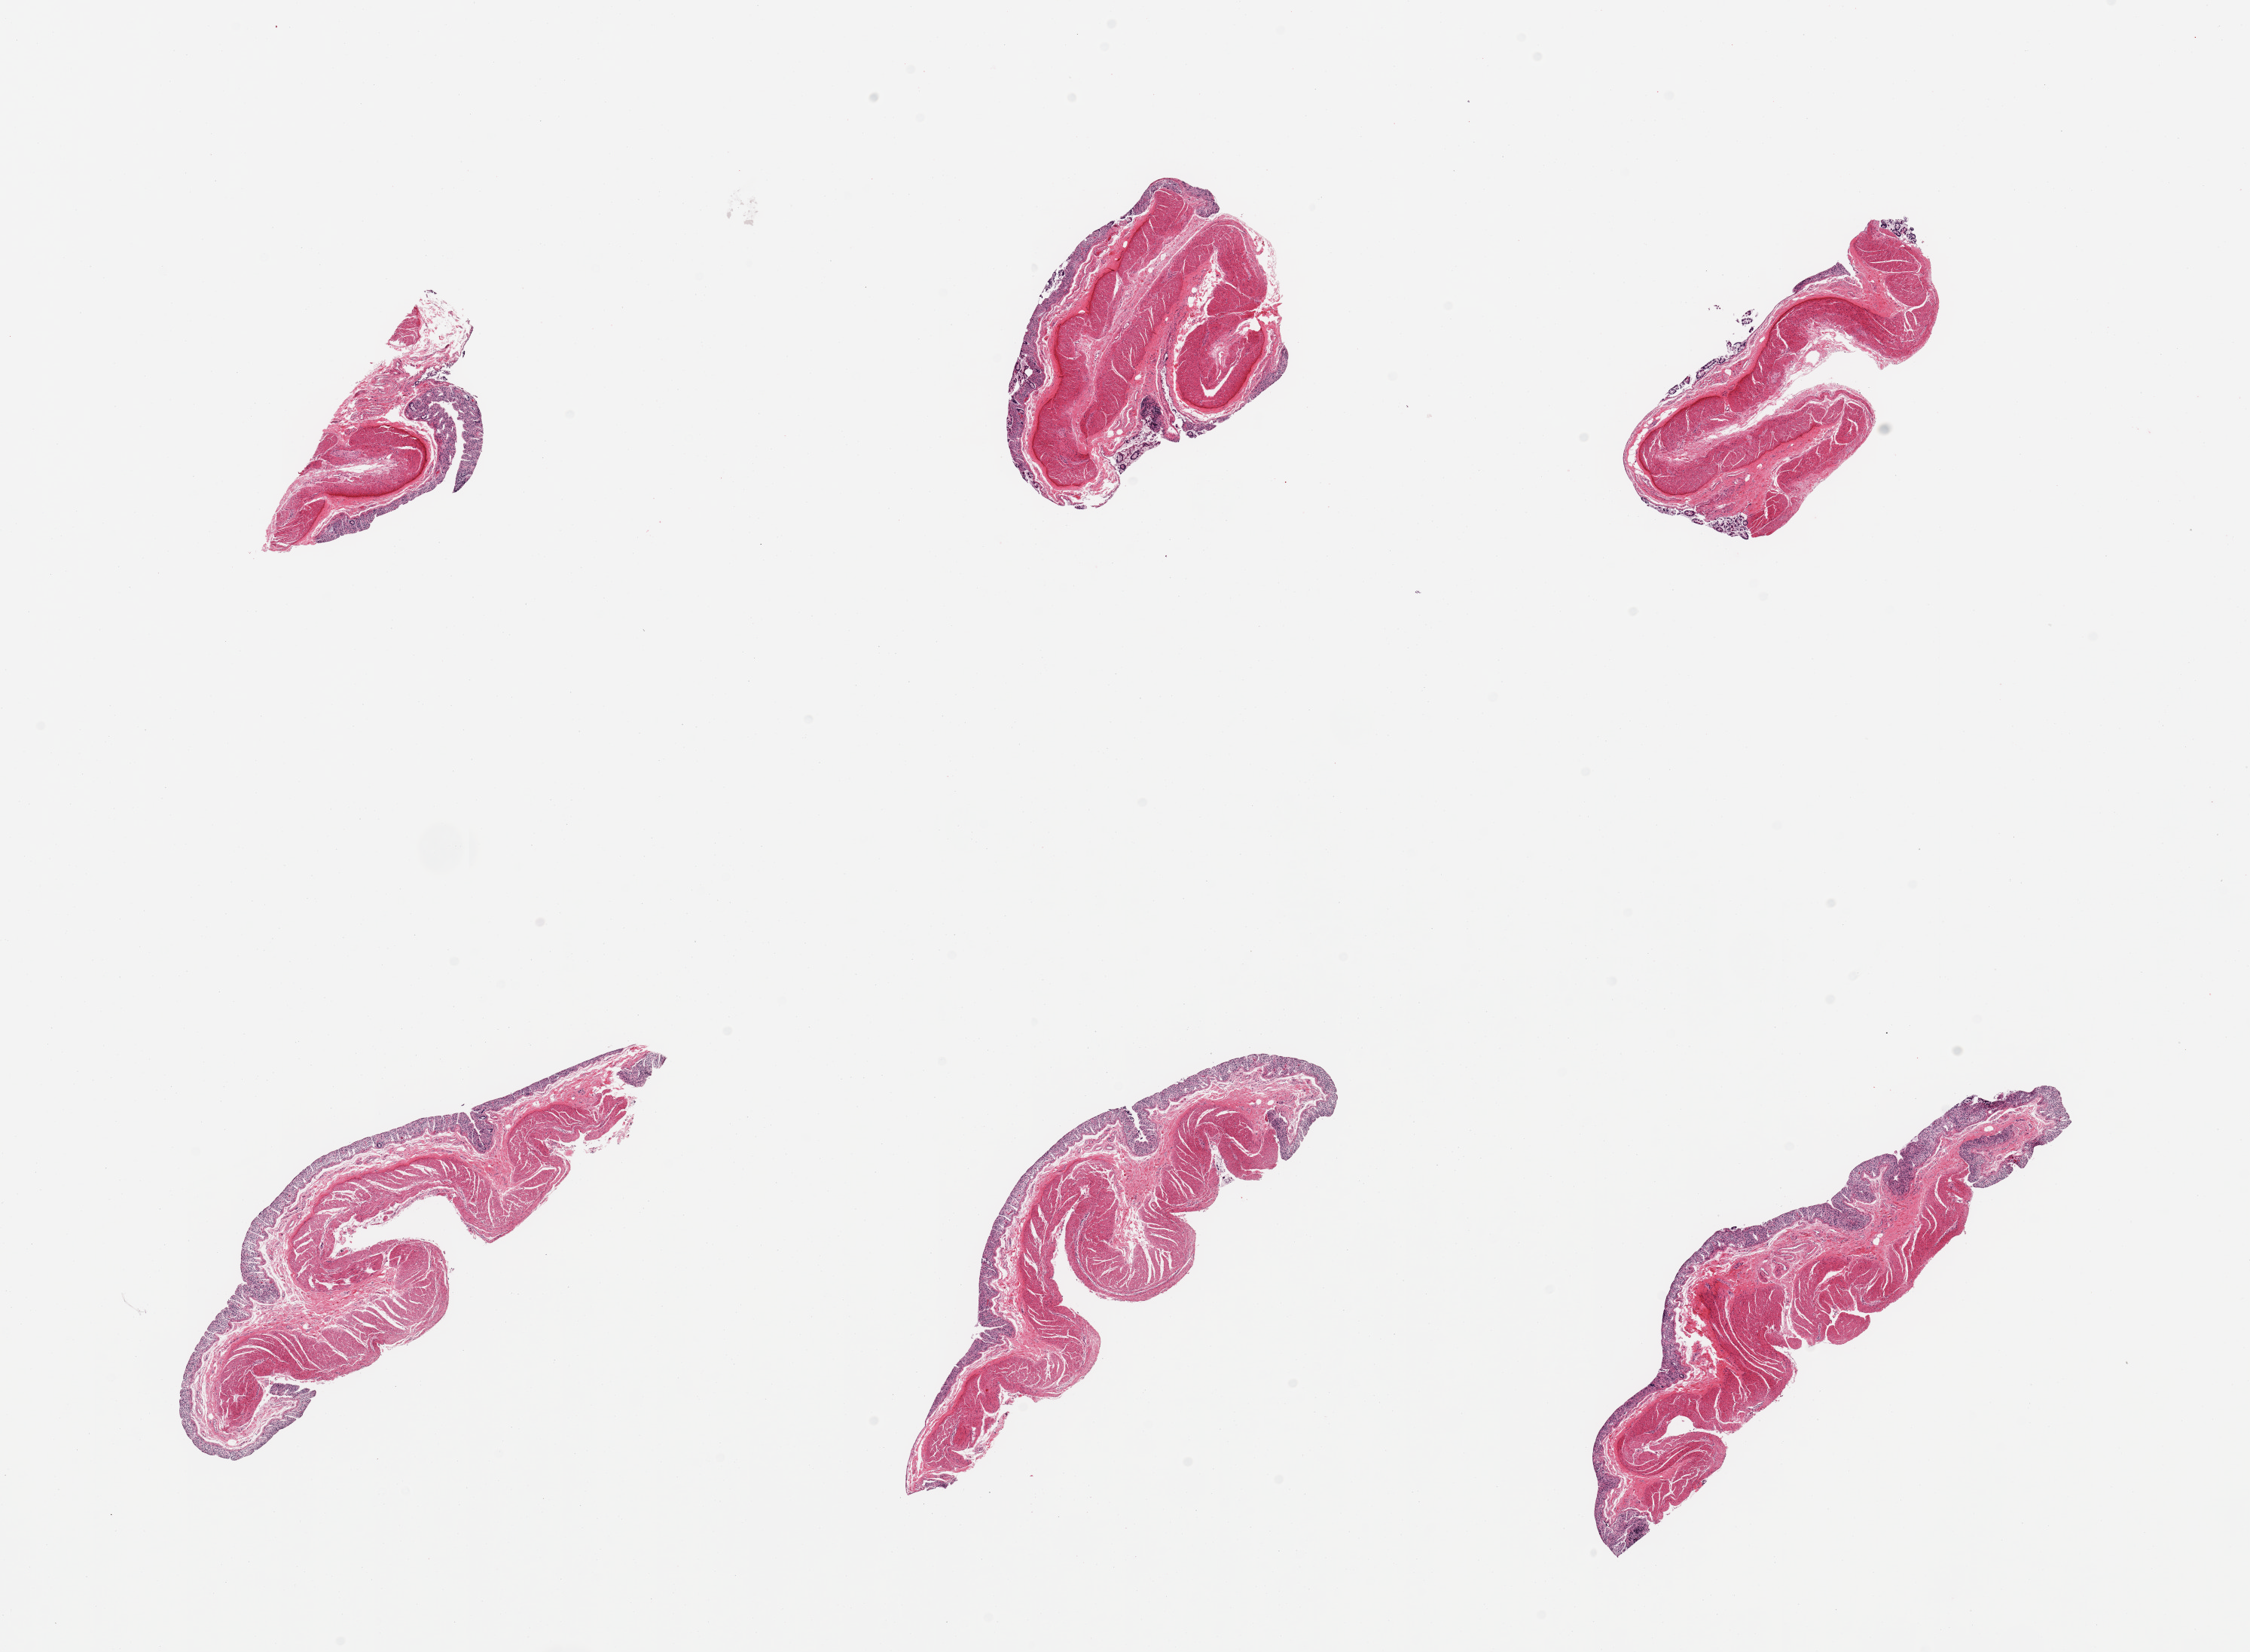
Digitized haematoxylin and eosin-stained section, a low-resolution overview of the entire scanned area, about 23.6 x 17.3 mm (from a 20x scan); PAXgene-fixed, paraffin-embedded tissue; sampled site (target tissue): transverse colon; tissue donor sample. Donor: male.
Pathologist's review note for this sample: 6 pieces; mucosa autolyzed [3], muscle intact [1].